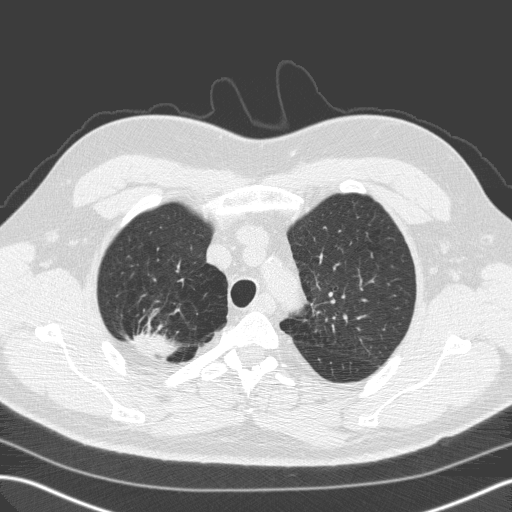
Low-dose screening chest CT, axial slice; baseline annual screen; lung window (W 1500 / L -600 HU); 2 mm slice thickness; 120 kVp. Male participant, aged 59 years at enrolment. Former smoker at enrolment.
• Expert-annotated lung lesion, bounding box (x1, y1, x2, y2) in pixels: (118, 314, 180, 366).
• The exam's reader record, not a measurement of the box and not confirmed to be the same lesion: non-calcified nodule or mass ≥4 mm, right upper lobe, 28 × 25 mm, spiculated (stellate) margins, soft tissue attenuation.
• Official screen result: positive, change unspecified: nodule(s) >= 4 mm or enlarging nodule(s), mass(es), or other non-specific abnormalities suspicious for lung cancer.
• Lung cancer was diagnosed 64 days after this screen: large cell carcinoma, NOS, right upper lobe, undifferentiated (G4), stage IA (AJCC 6th edition), 25 mm at pathology.